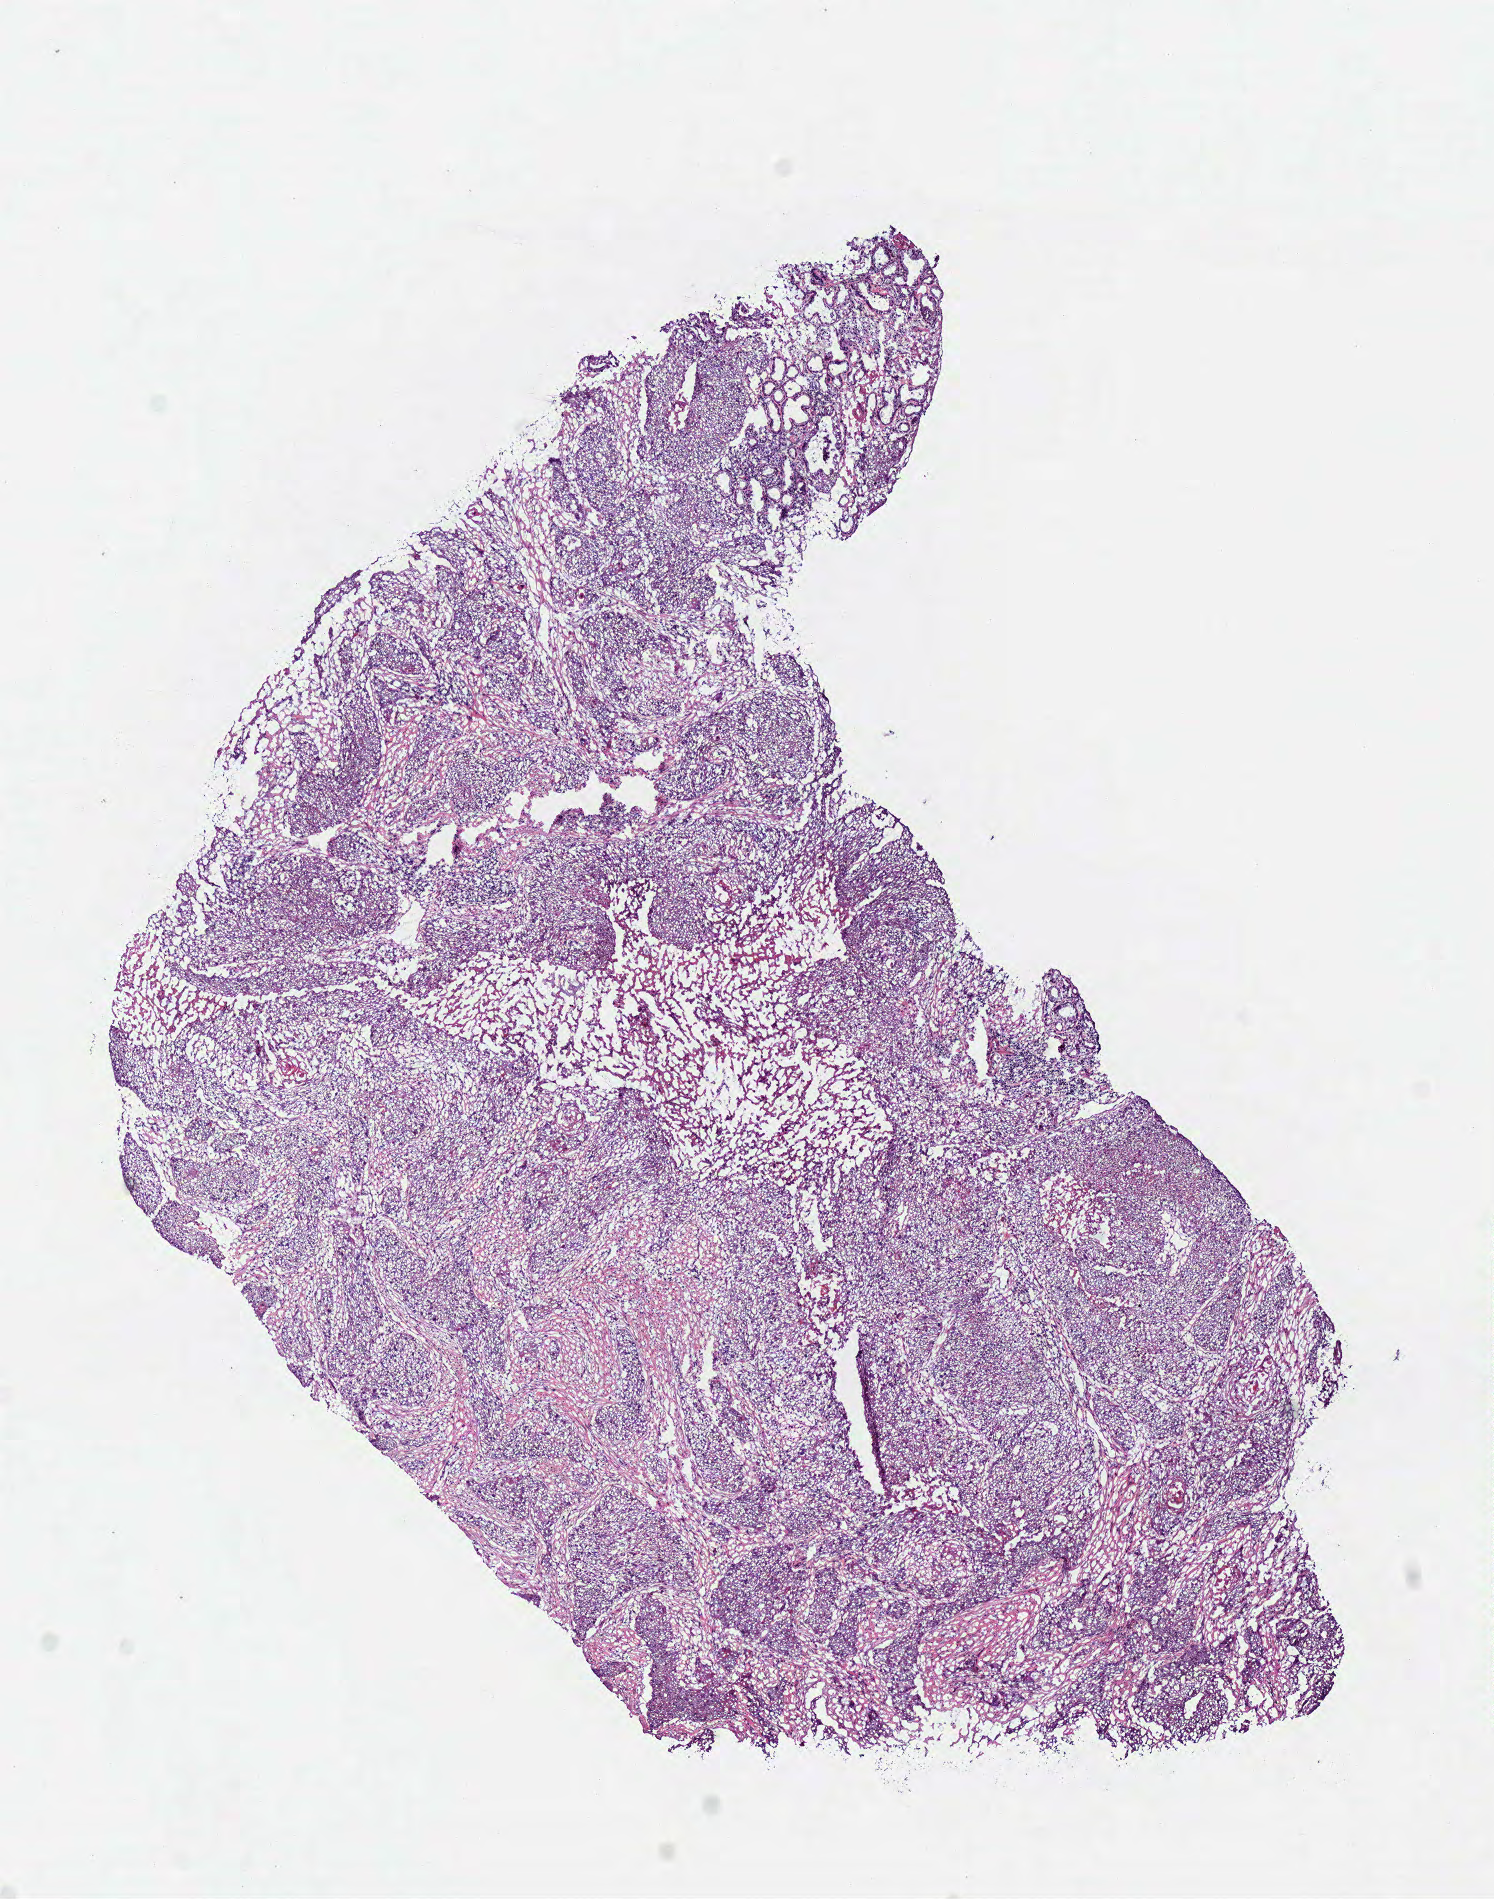
H&E-stained whole-slide image — a low-resolution overview of the entire scanned area, about 5.9 x 7.5 mm (from a 40x scan); frozen section from the top of the tissue portion; head and neck, primary tumour sample. Male, age 64 years at initial diagnosis. Histologic grade: G2 (moderately differentiated). Composition of this section per pathologist review: tumour cells 75%, tumour nuclei 80%, normal cells 5%, stromal cells 10%, necrosis 10%.
• lymph nodes positive (case pathology): 2 of 47 examined
• diagnosis: Squamous cell carcinoma, NOS